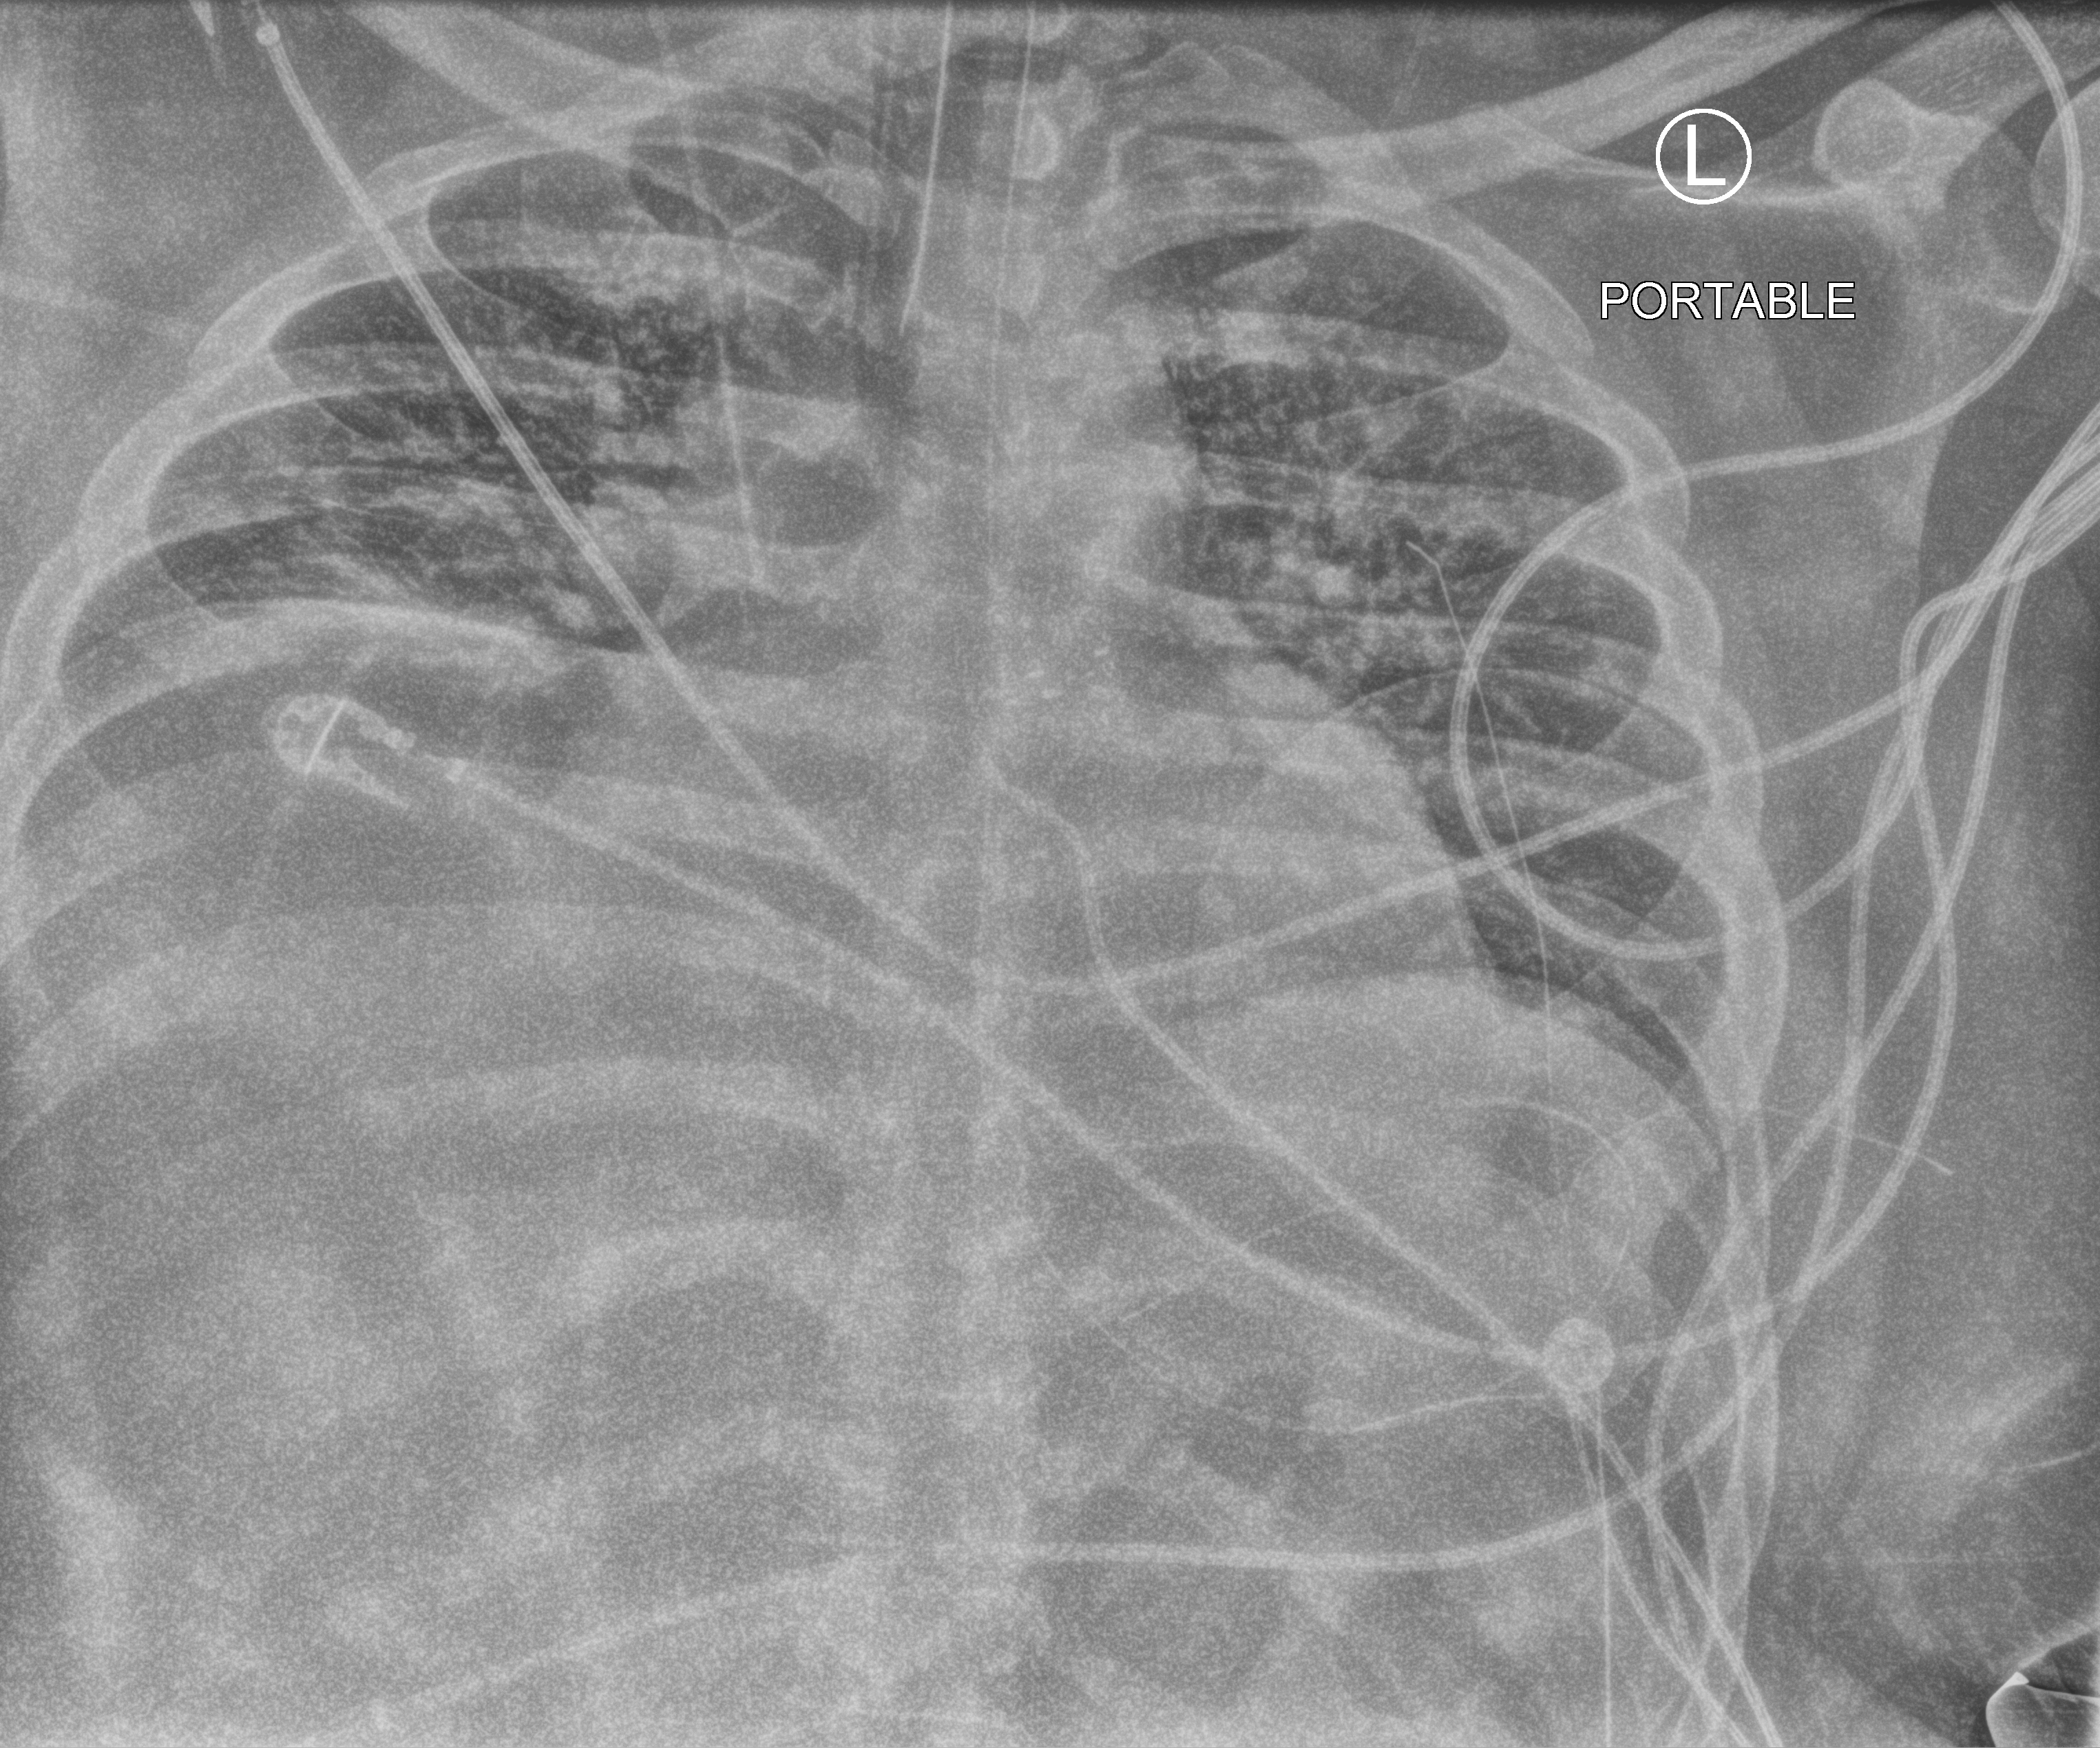
Chest X-ray (portable). Male patient hospitalised with COVID-19, age 18–59 years.
Admission-level facts for this patient (not findings on this image; timing relative to this image not recorded):
- length of hospital stay: 69 days
- admitted to intensive care during this hospital stay: yes
- mechanically ventilated during this hospital stay: yes